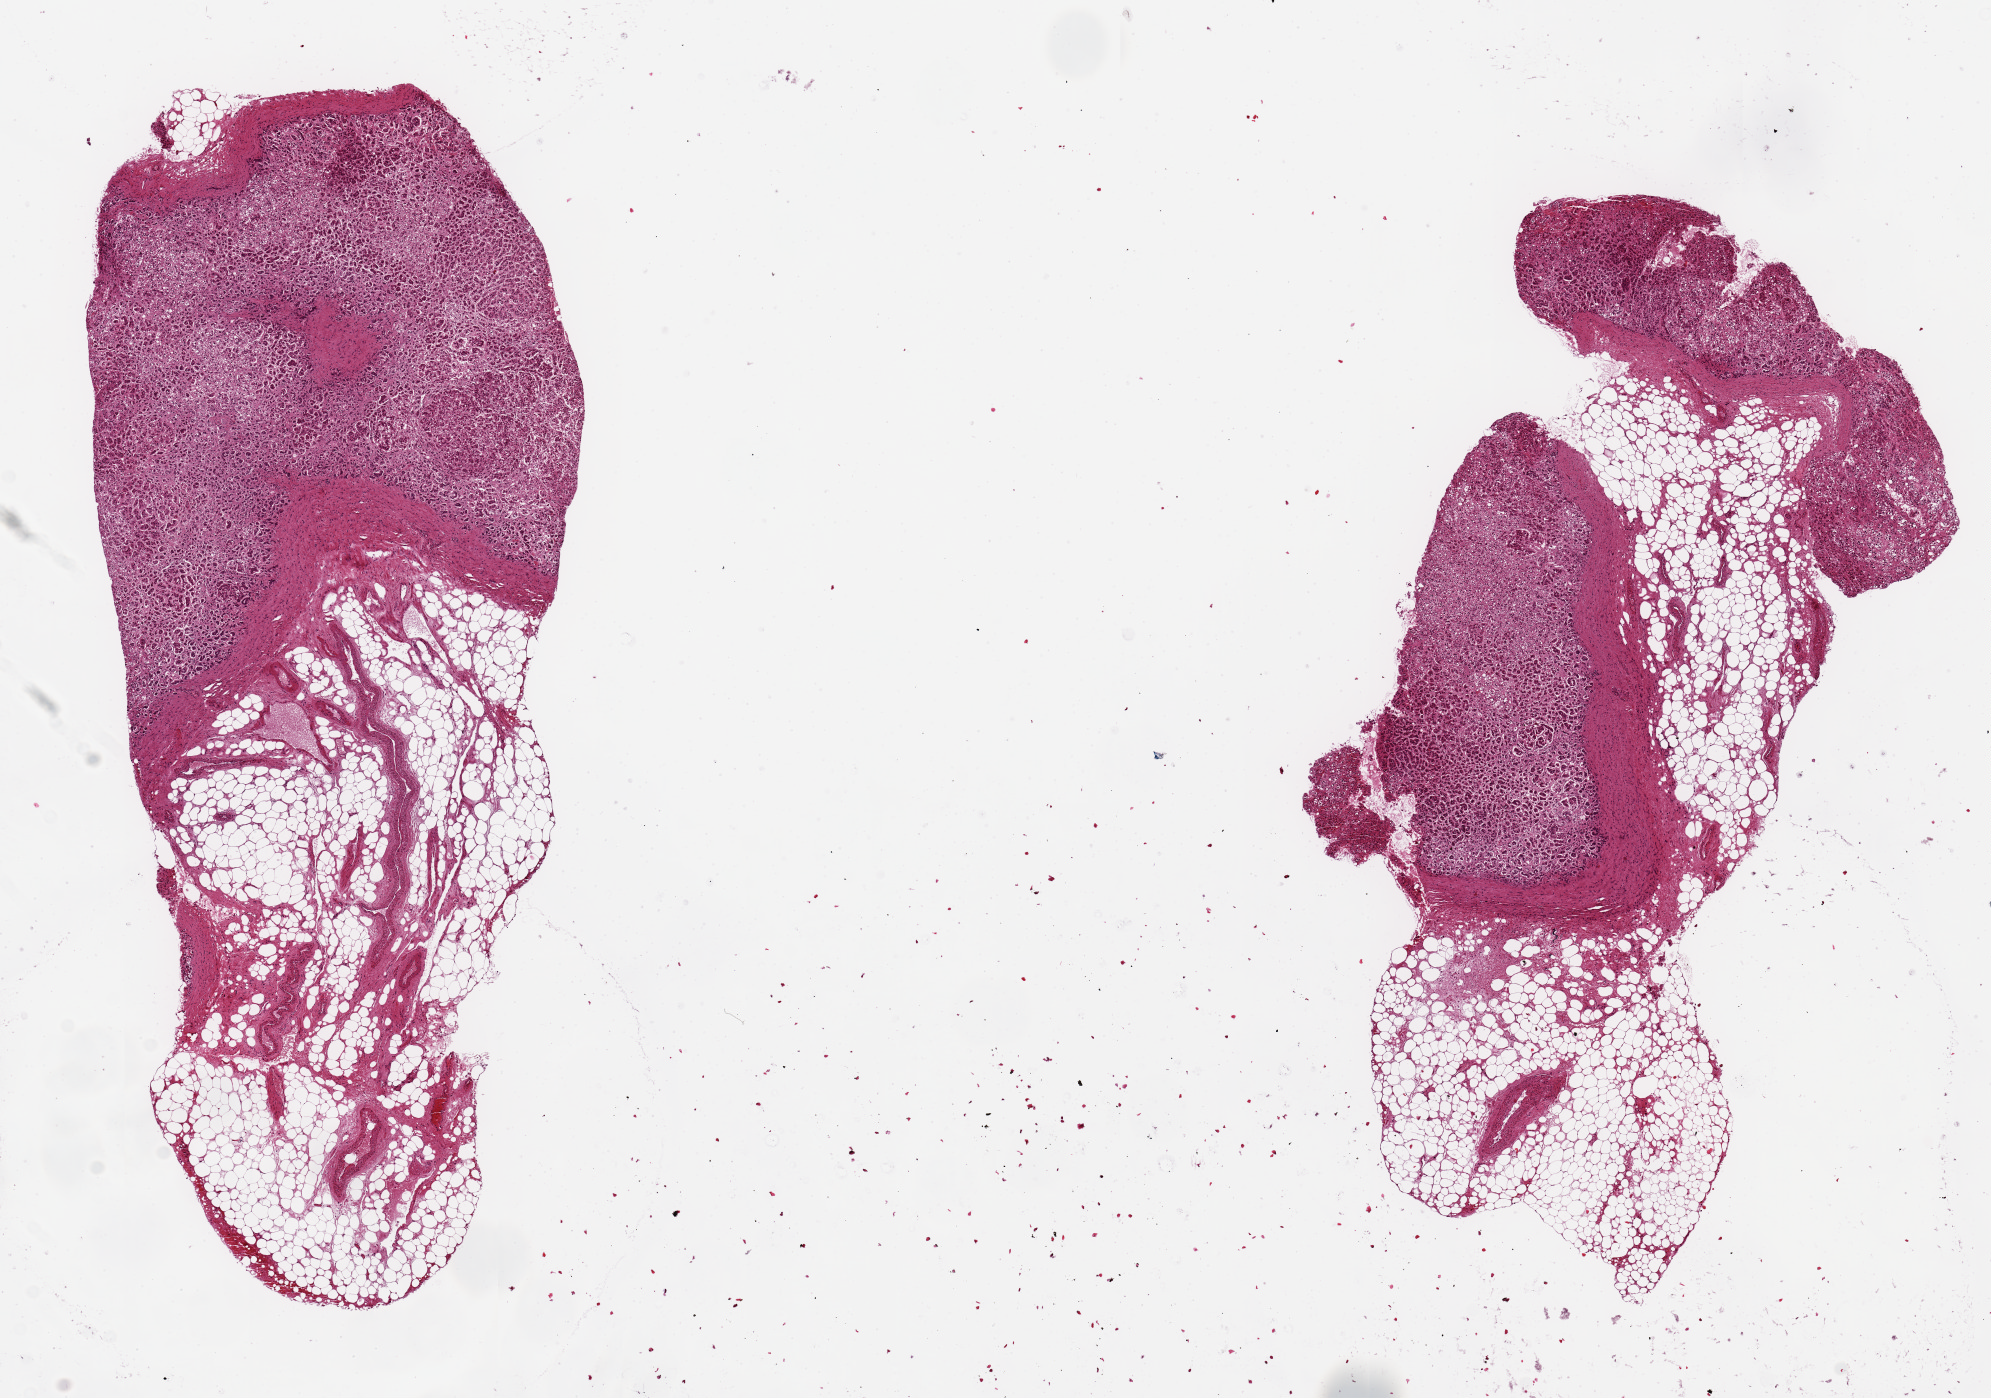
Whole-slide image, H&E stain — a low-resolution overview of the entire scanned area, about 15.8 x 11.1 mm (slide scanned at 20x). PAXgene-fixed paraffin-embedded (PFPE) section. Section of adrenal gland (target tissue). Tissue donor sample. Donor: male.
- reviewer comment on this tissue sample: 2 pieces, 10x4 & 9x4mm; ~40-50% fat, rest is all cortex